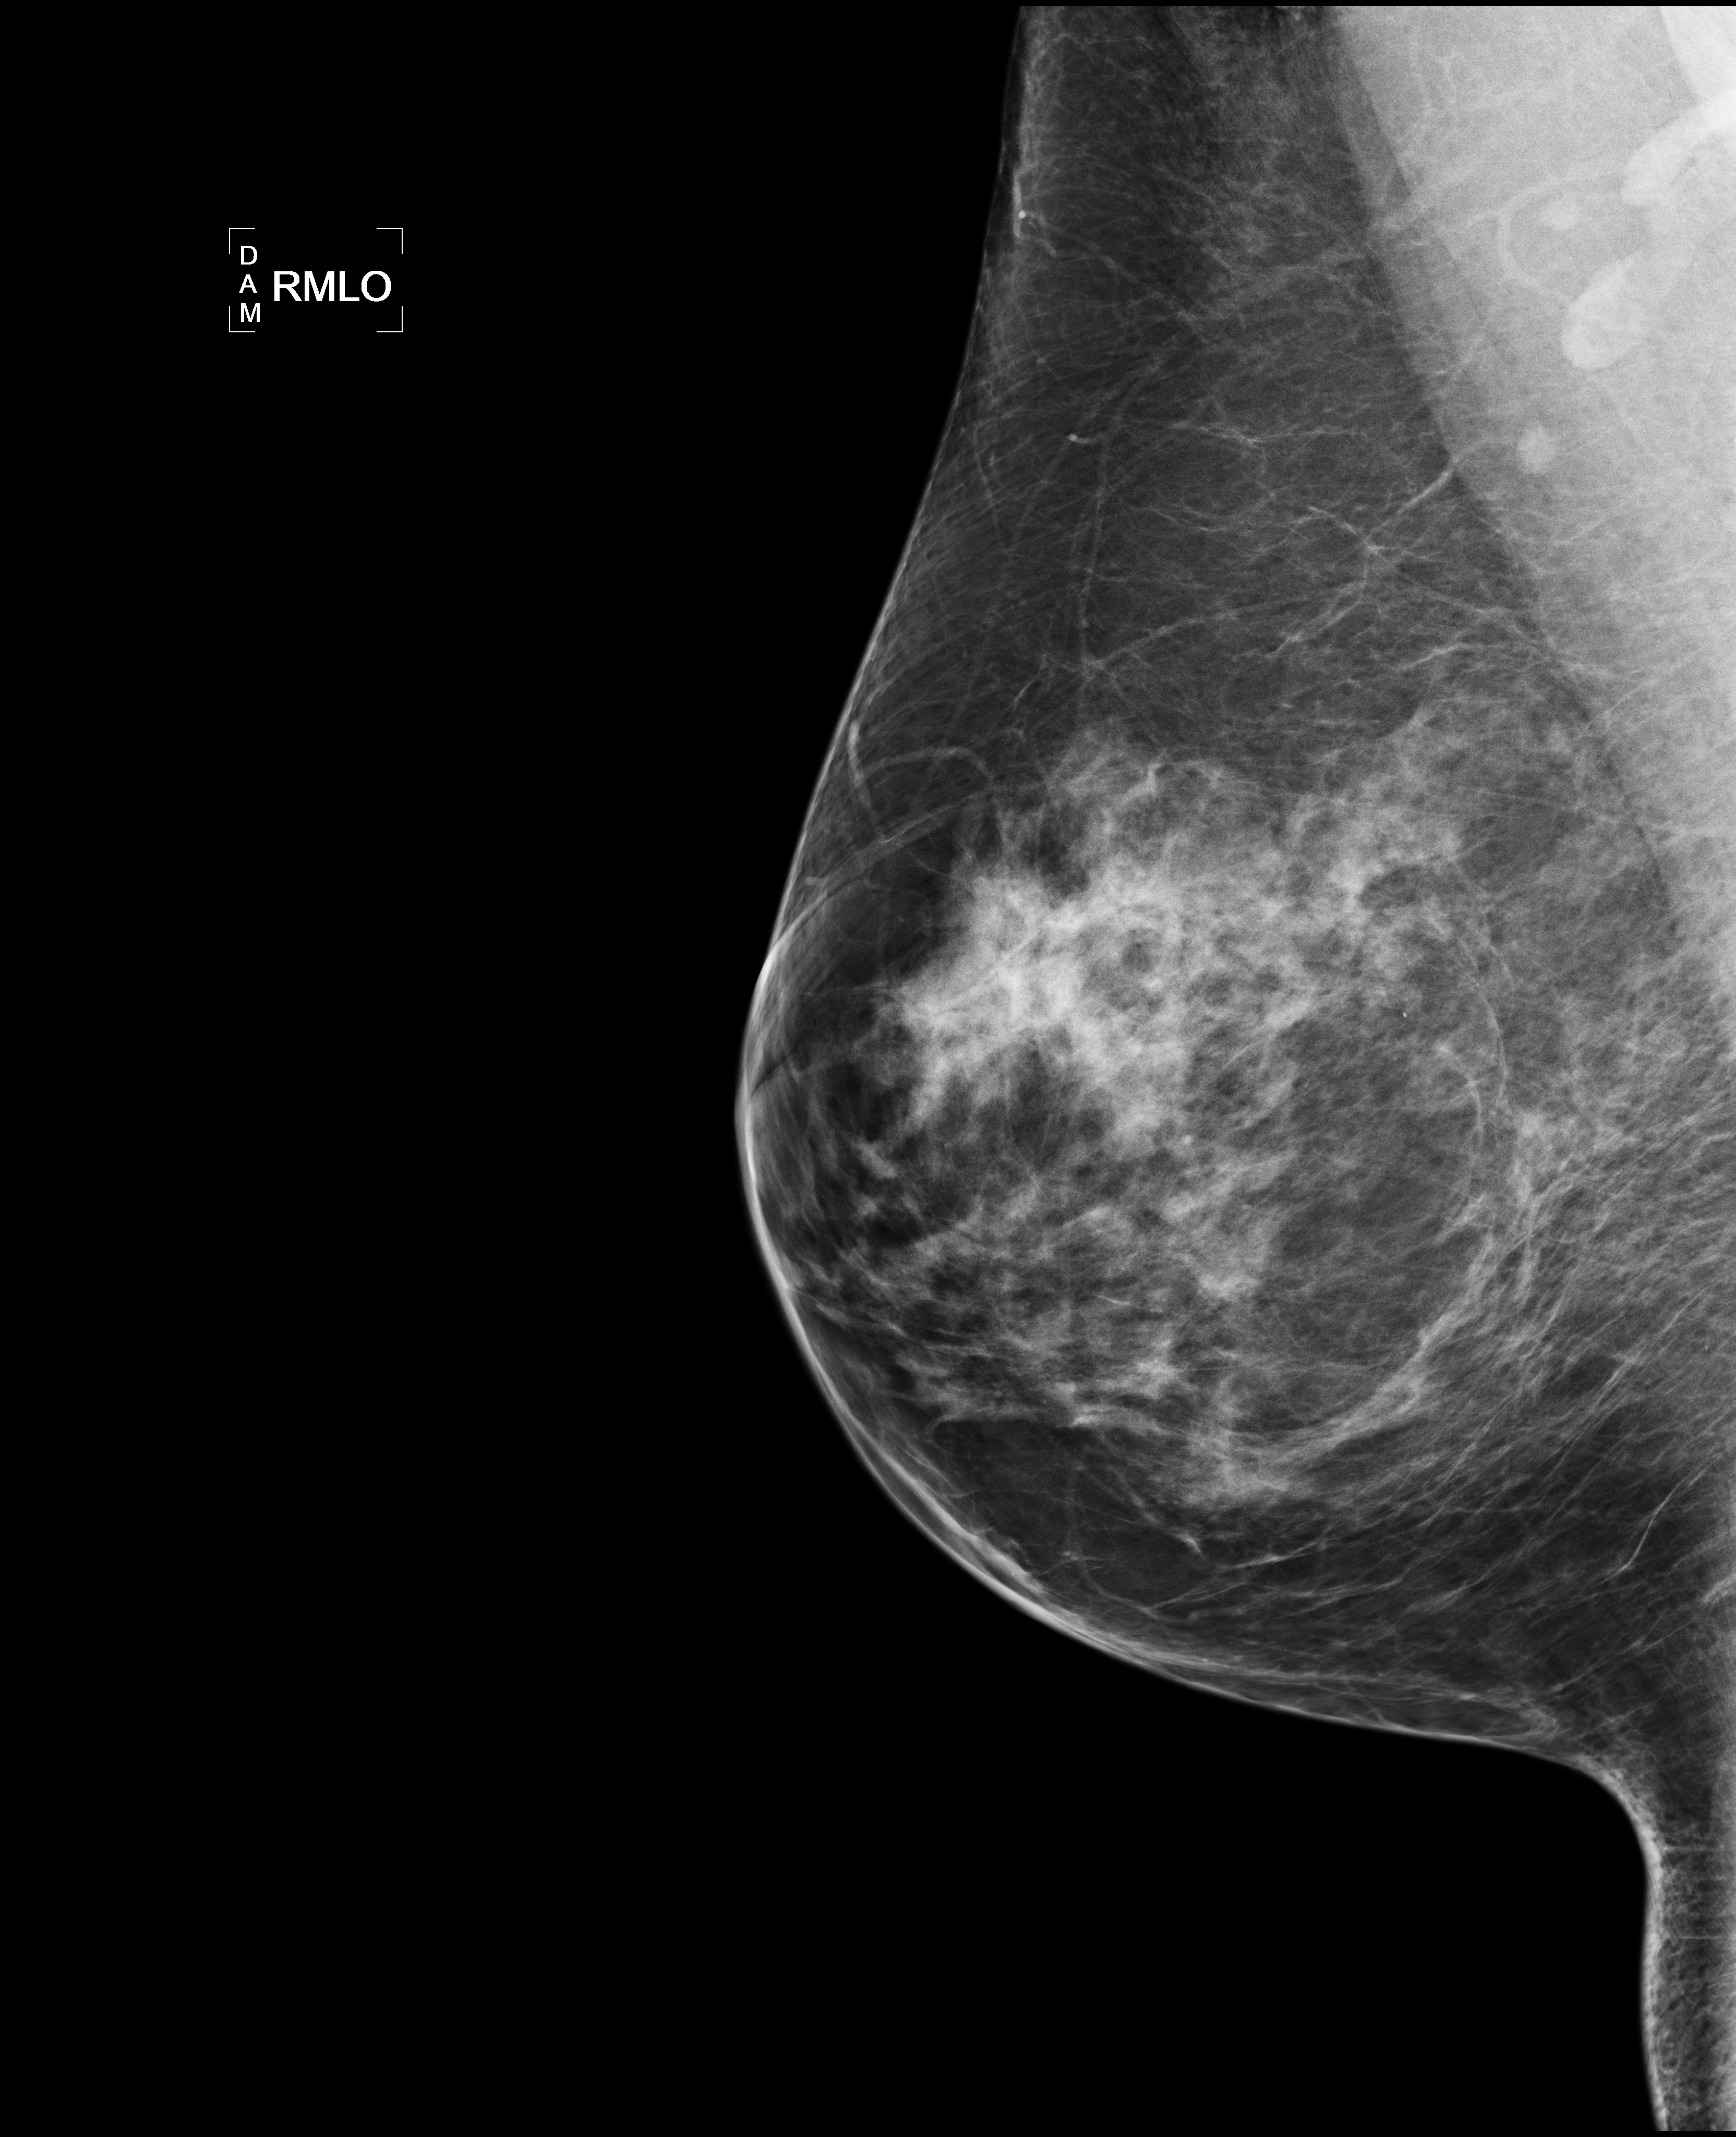
Mammogram, right breast, MLO view; patient in her 50s.
Pathology recorded for this patient (not read from this image): pathology diagnosis: Invasive ductal CA (left breast); receptor status (as recorded): ER pos, PR pos (weak), HER2 neg; Ki-67 (as recorded): intermed prolif; pathology report notes: re-bx [date] was scar tissue from RT rx.